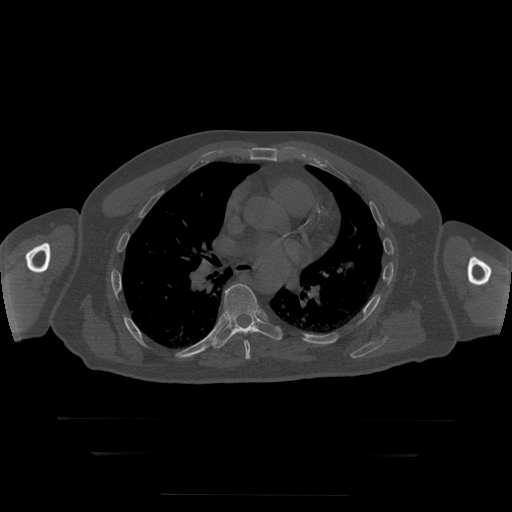
CT including the spine, one axial slice; position 172 of 397 along the scan axis; reconstruction kernel STANDARD; 120 kVp; bone window (W 1800 / L 400 HU); 512 × 512 image matrix, field of view 510 × 510 mm. Patient age 73 years. From the clinical record (not read from this slice): primary cancer: prostate.
Annotated regions visible in this slice (semi-automatic segmentation, software-assisted and operator-edited):
- T7 vertebra: bounding box <244,340,251,360> (left, top, right, bottom; pixels)
- T8 vertebra: <211,284,283,349>